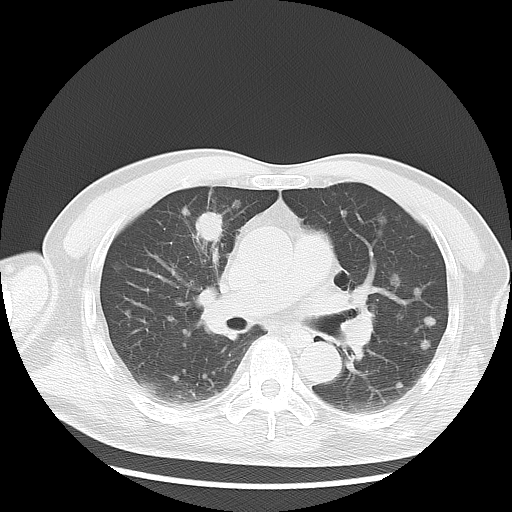
Chest CT, one axial slice; slice 11 of 36 in the series (ordered by position); reconstruction kernel LUNG; 120 kVp; lung window (W 1500 / L -600 HU); 512 × 512 image matrix. Male patient, age 57 years. Case-level facts recorded for this patient, not image findings: clinical TNM (as recorded): T2 N3 M1a.
Structures marked on this image (bounding box drawn by a radiologist):
- lung tumour (recorded histology: adenocarcinoma): box from (x=192, y=207) to (x=225, y=248) px